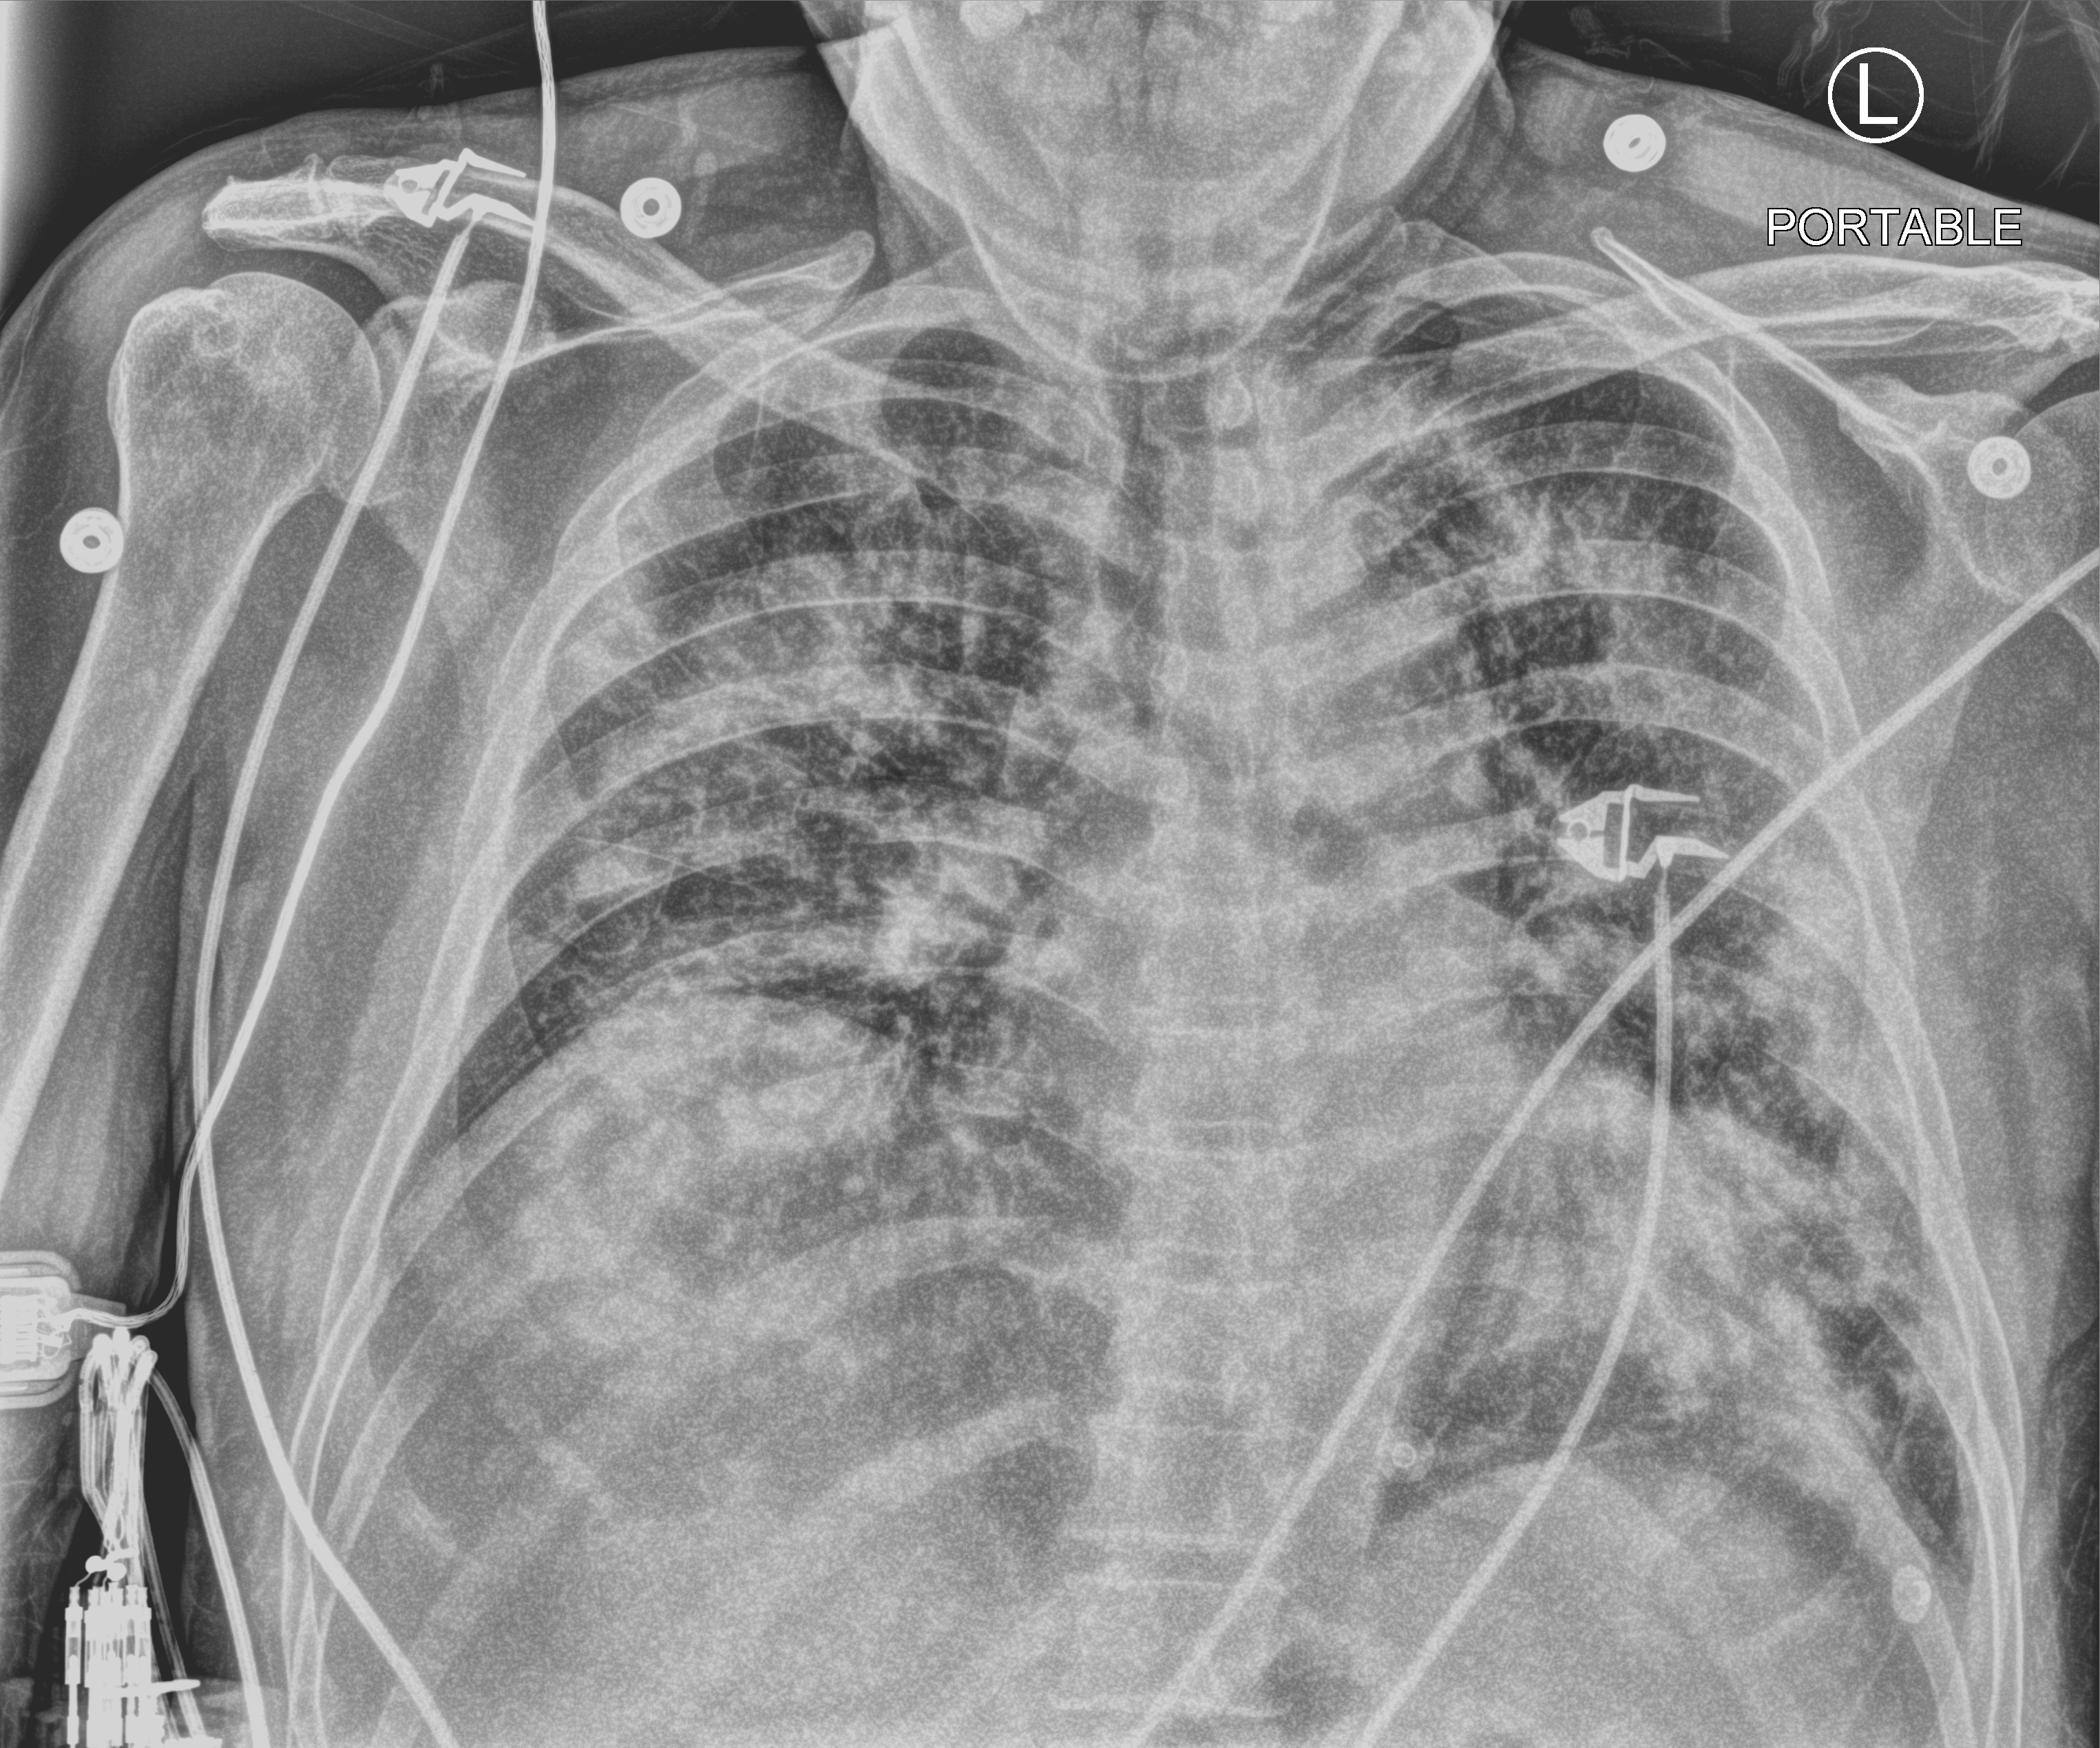
Chest X-ray (portable), anteroposterior (AP) projection. Male patient hospitalised with COVID-19, age 60–74 years.
Admission-level facts for this patient (not findings on this image; timing relative to this image not recorded): other chronic lung disease (admission record): no; length of hospital stay: 10 days; chronic kidney disease (admission record): no.